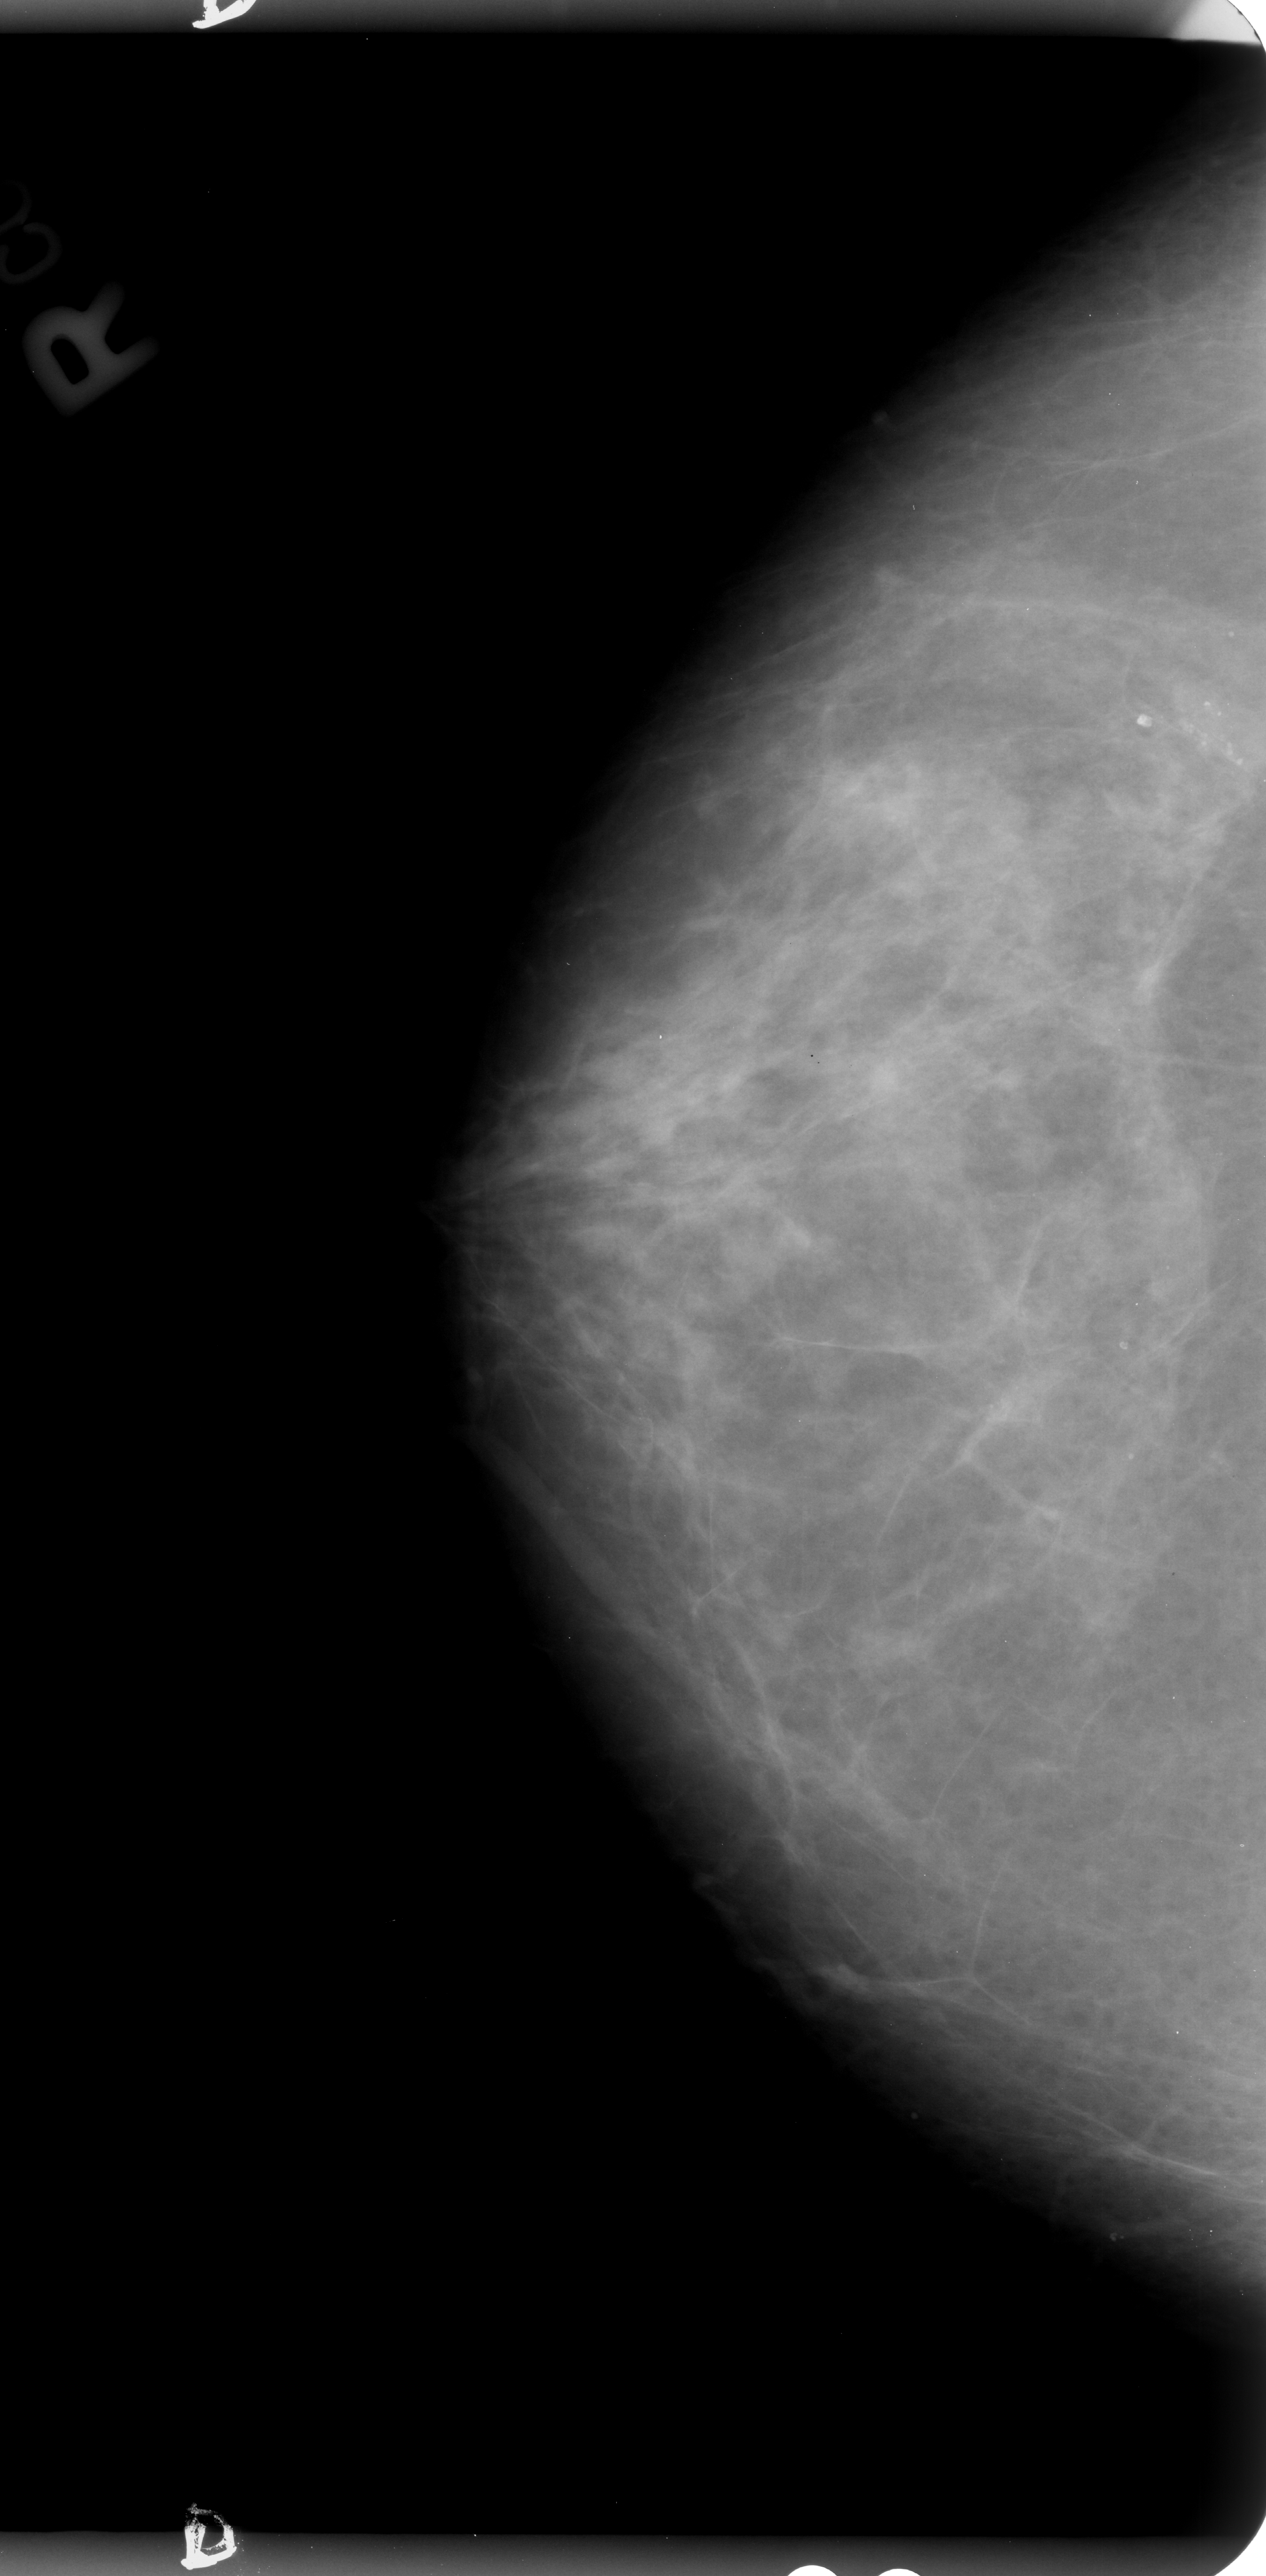
Scanned film-screen mammogram. Right breast. CC view. BI-RADS breast density category 2 (scale 1–4). 1266 × 2576 image matrix.
Expert-marked regions of interest on this image (one box per marked abnormality):
- calcifications, morphology pleomorphic, distribution clustered; BI-RADS assessment category 4; pathology result (as recorded, not read from the image): benign: bounding box <1143,650,1263,791> (left, top, right, bottom; pixels)